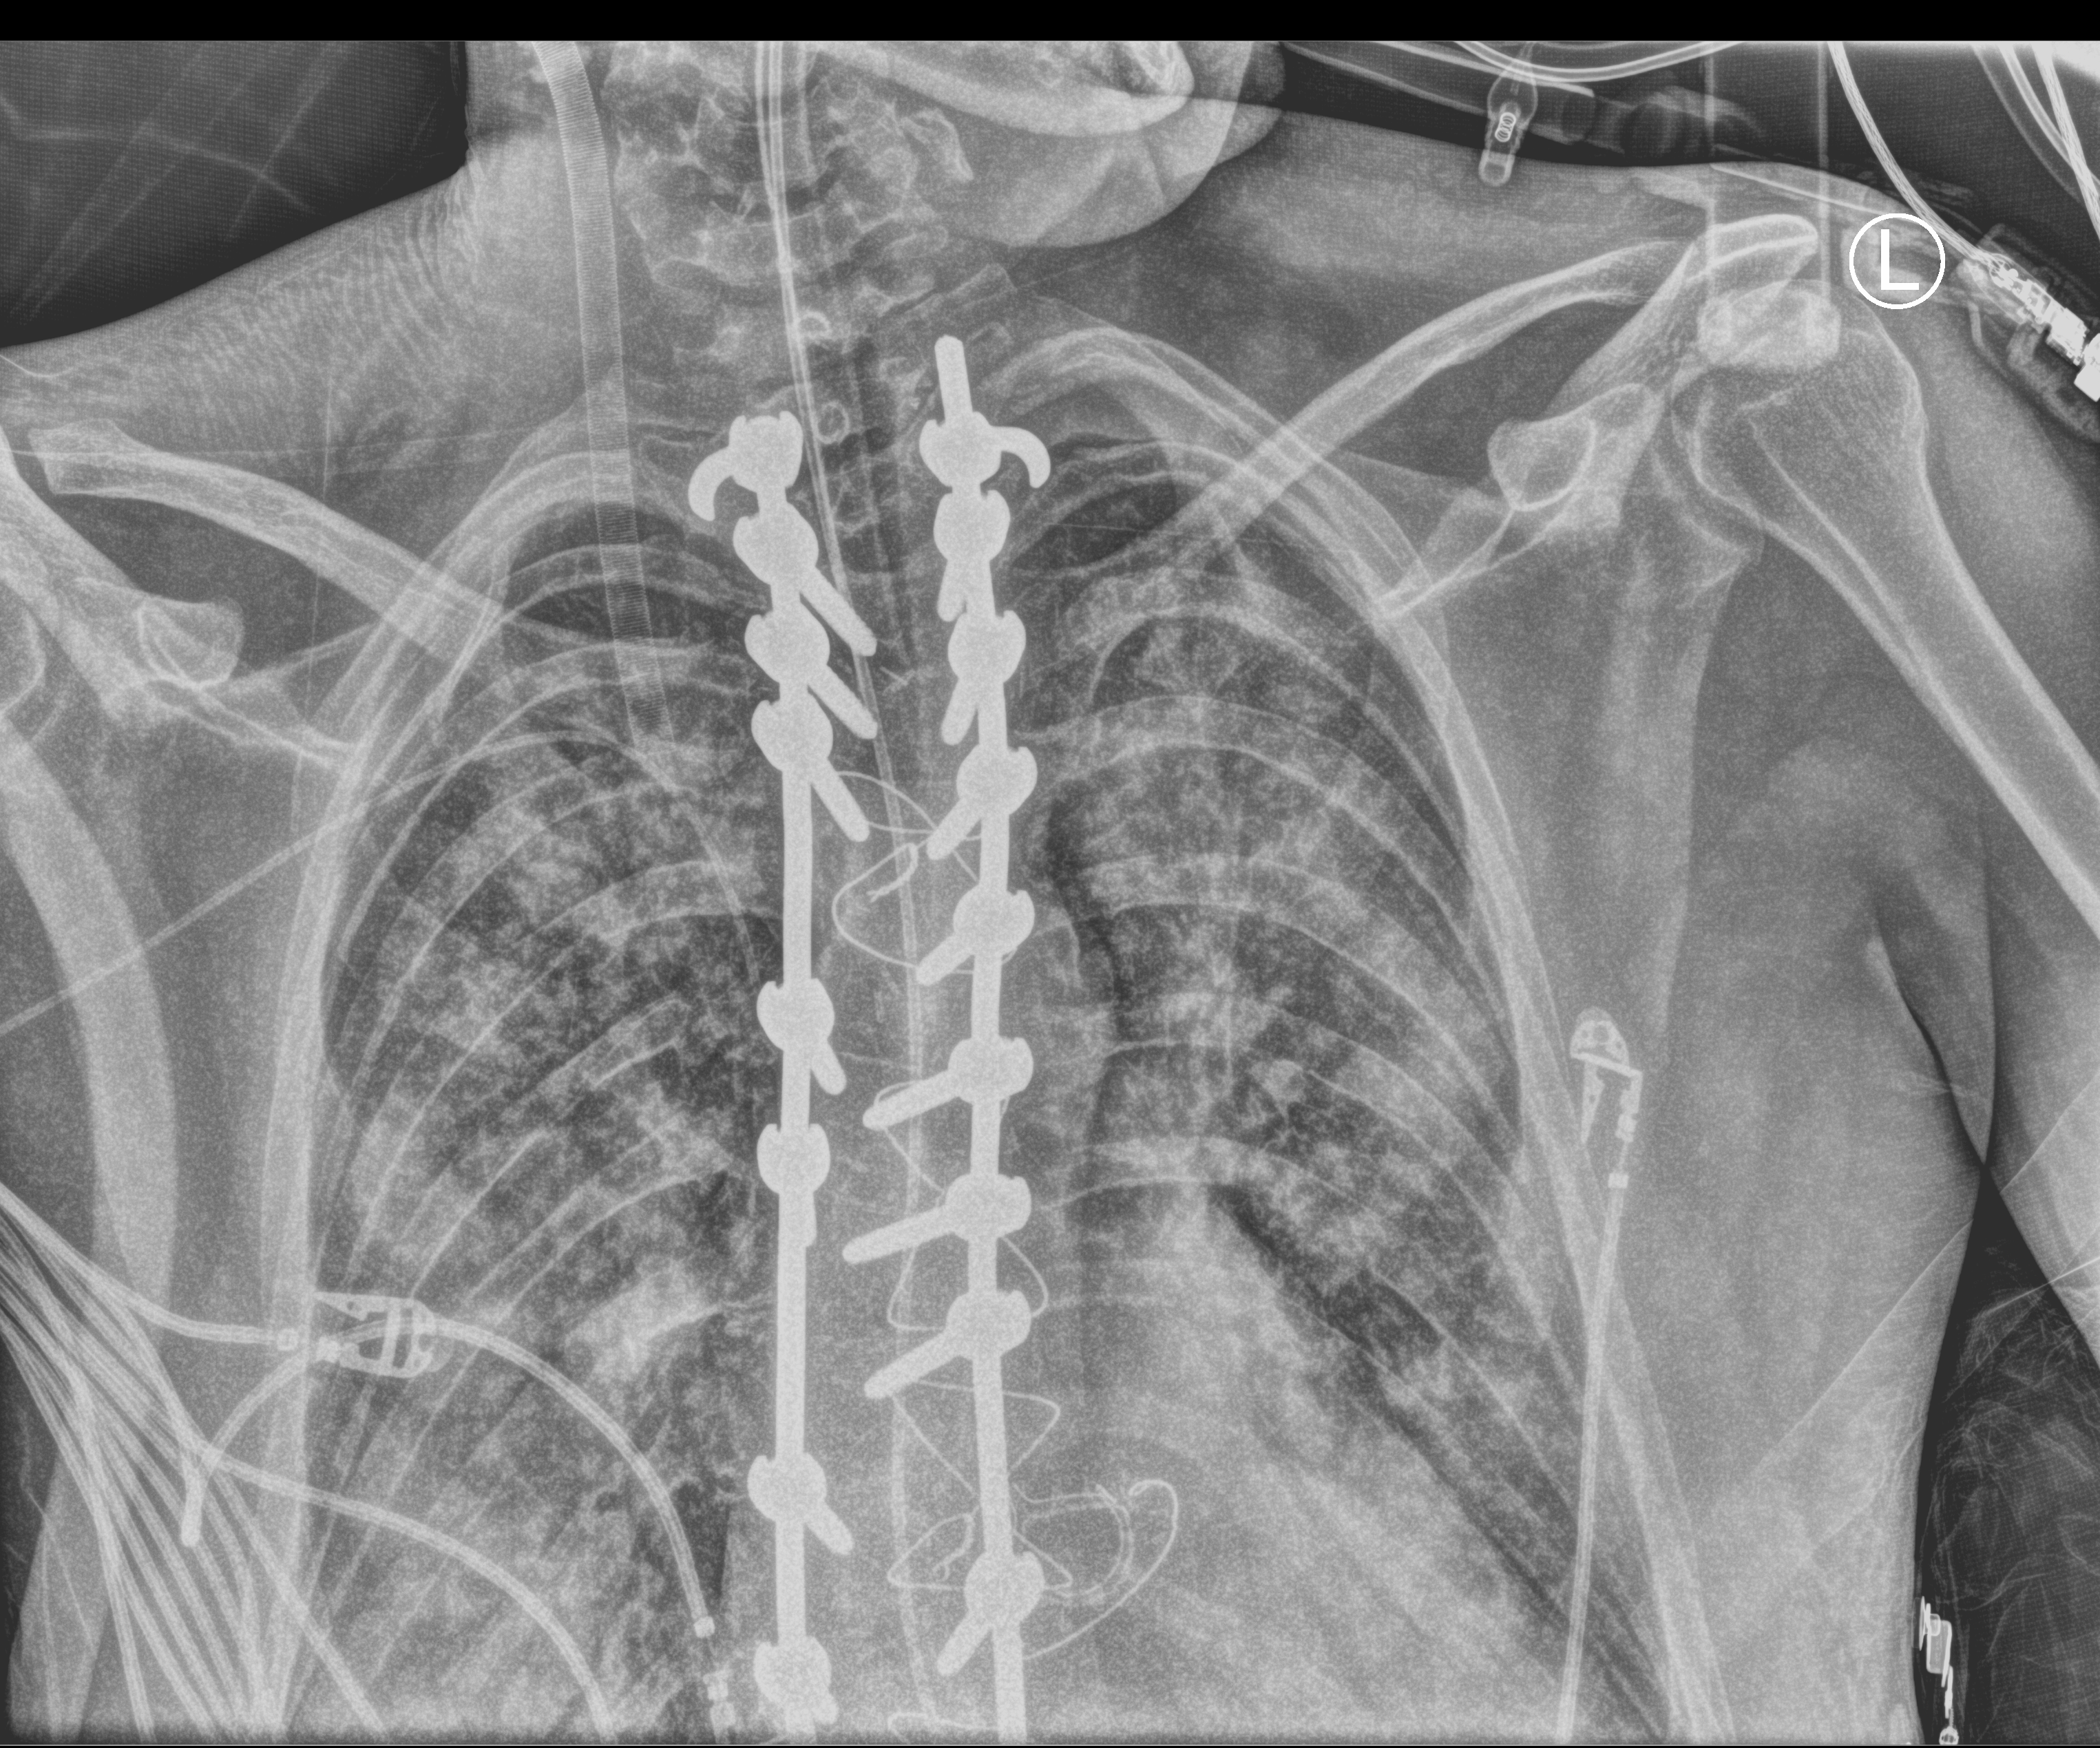
Chest radiograph (computed radiography), anteroposterior (AP) projection. Adult patient hospitalised with COVID-19, age 18–59 years.
Admission-level facts for this patient (not findings on this image; timing relative to this image not recorded):
- mechanically ventilated during this hospital stay: yes
- admitted to intensive care during this hospital stay: yes
- chronic kidney disease (admission record): no